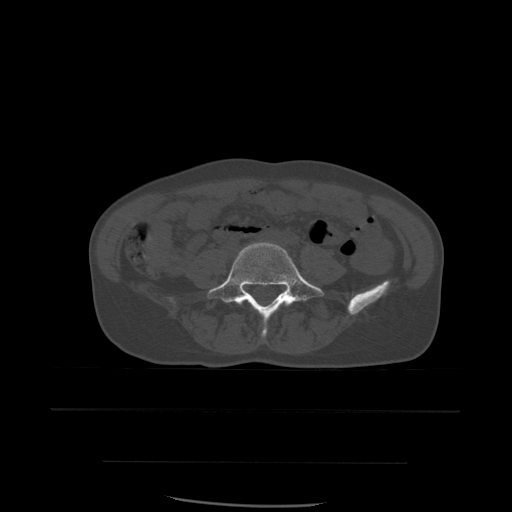
CT including the spine, one axial slice. Slice 152 of 574 in the series (ordered by position). Bone window (W 1800 / L 400 HU). 512 × 512 image matrix, field of view 392 × 392 mm. Patient age 48 years. Case-level facts recorded for this patient, not image findings: primary cancer: lung; vertebrae with lytic lesions (as recorded): T11.
Structures marked on this image (semi-automatically segmented with operator editing):
- L5 vertebra: bounding box <207,242,324,337> (left, top, right, bottom; pixels)